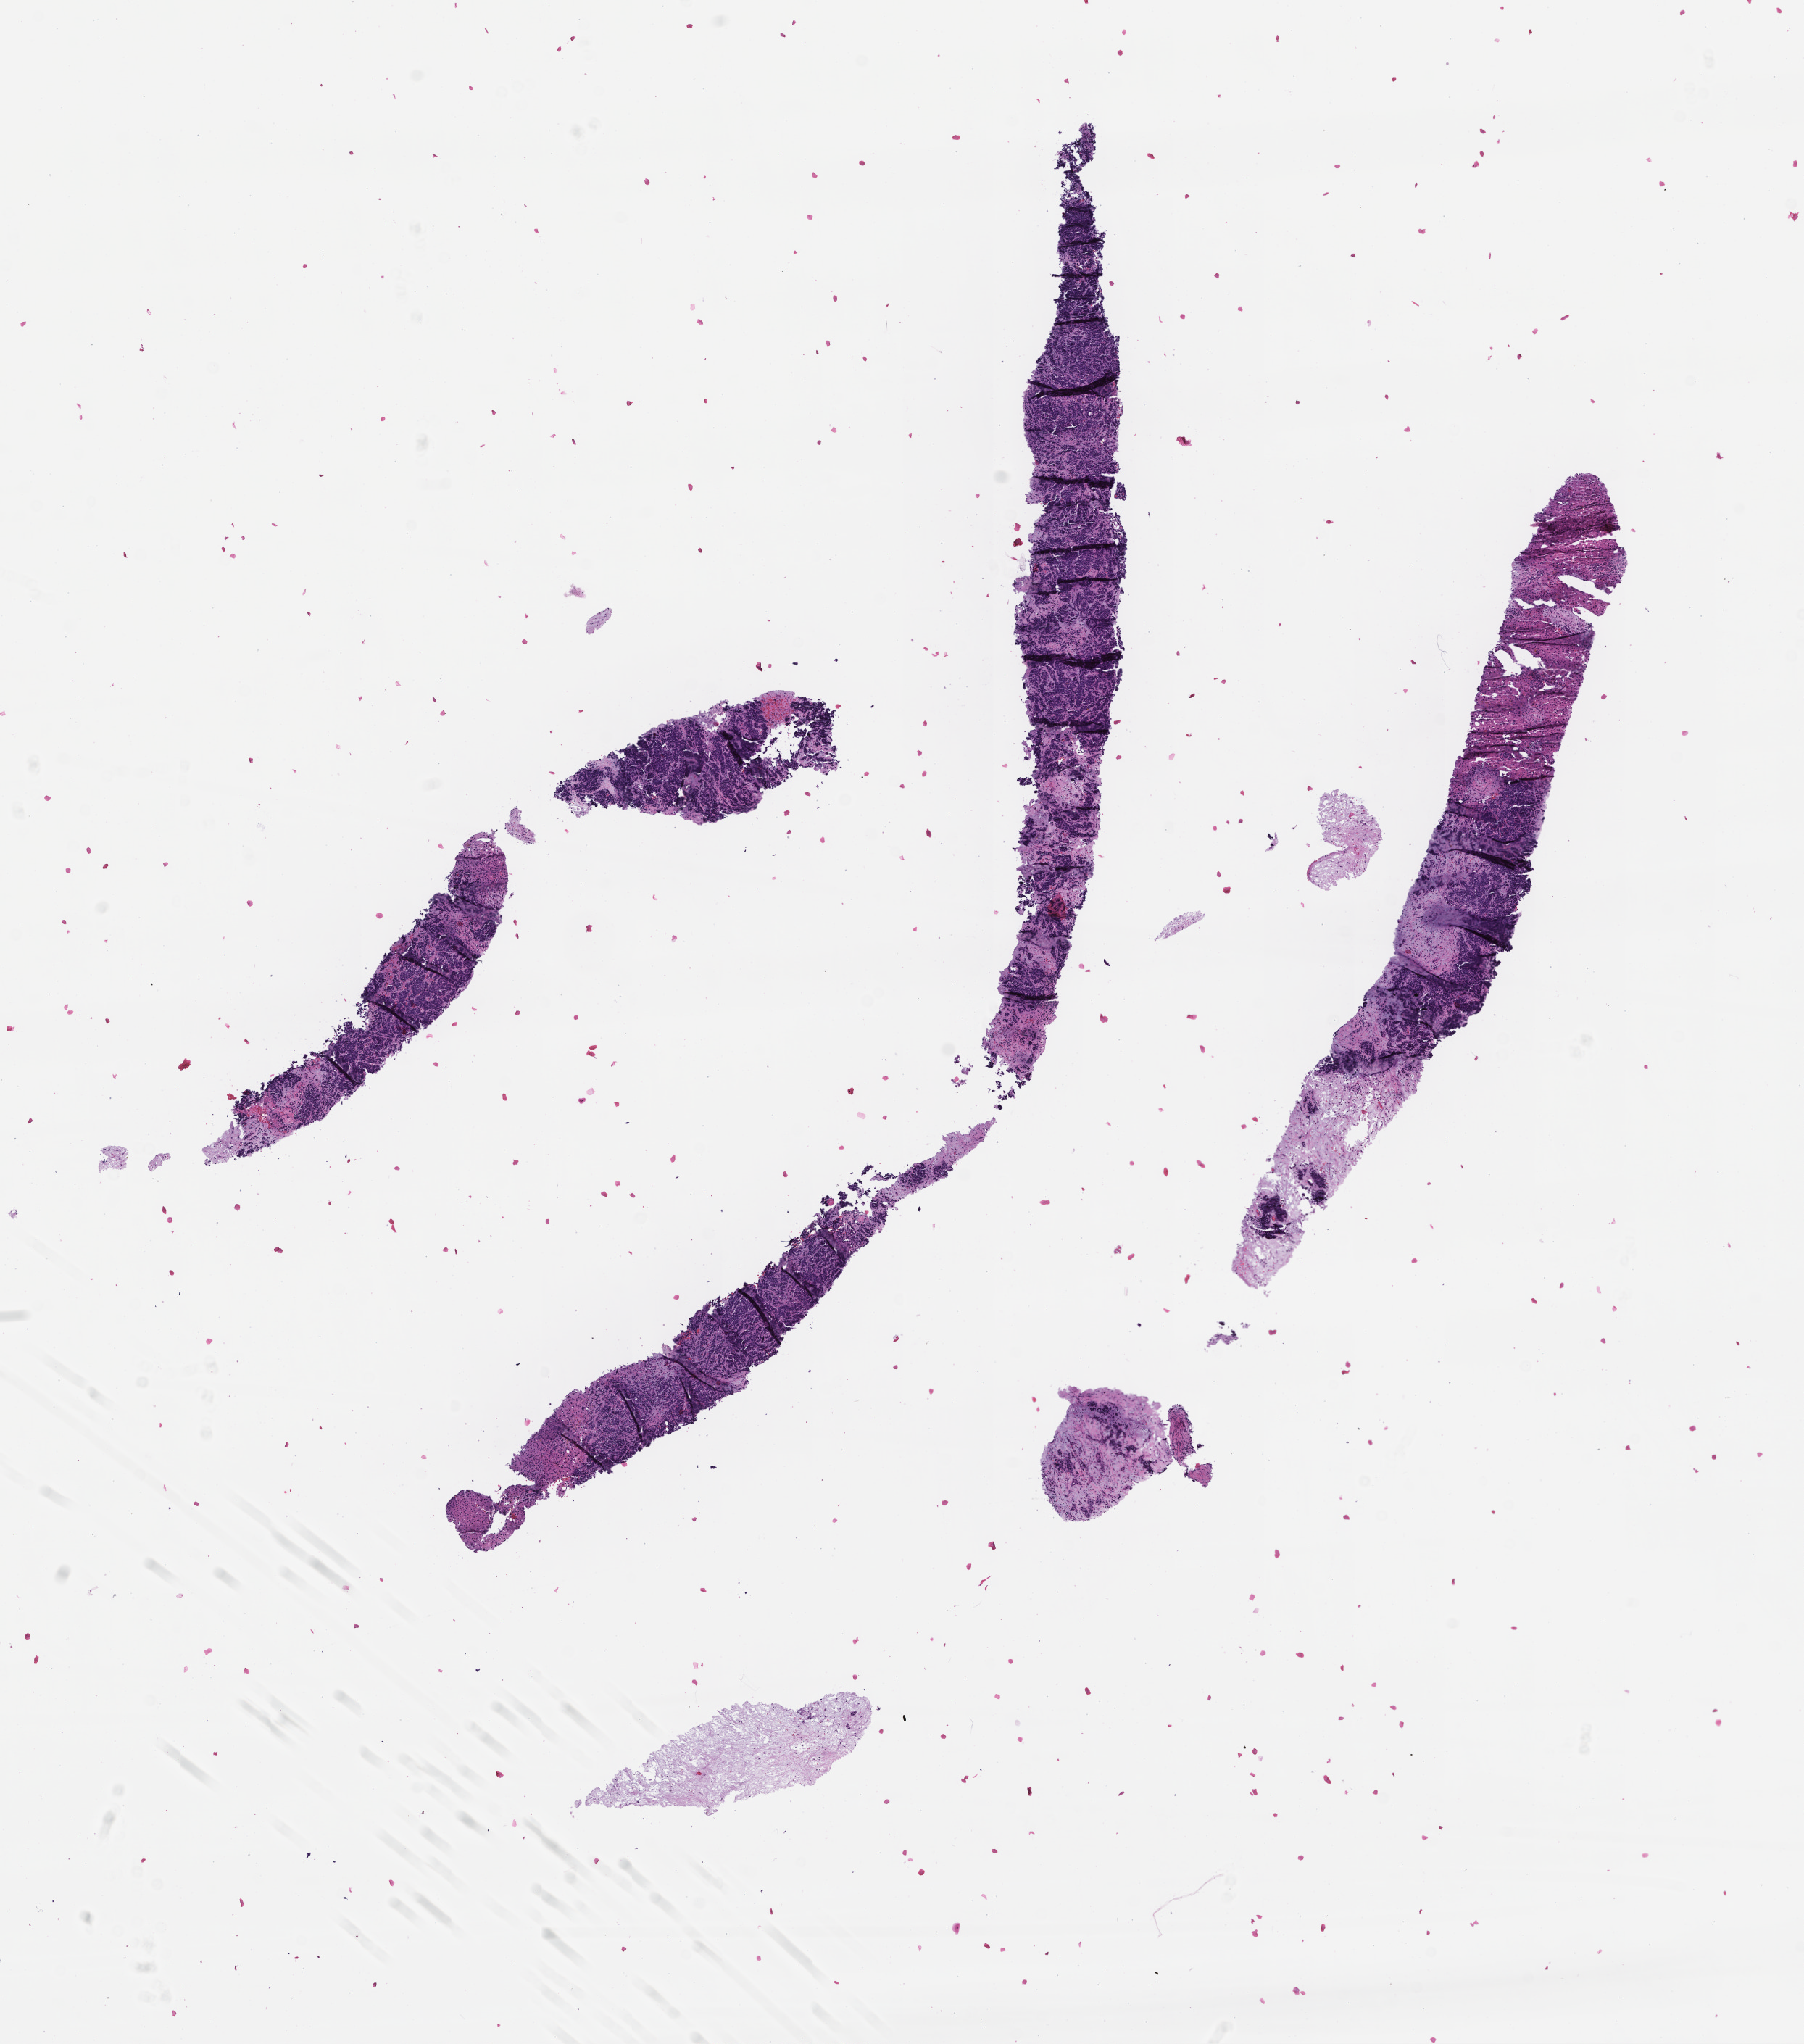
Whole-slide image, haematoxylin and eosin stain — shown as a low-resolution overview of the whole scanned area (about 10.1 x 11.4 mm), FFPE section. Male patient.
- this section: metastatic tumor tissue
- primary diagnosis of the patient: Small Cell Lung Carcinoma